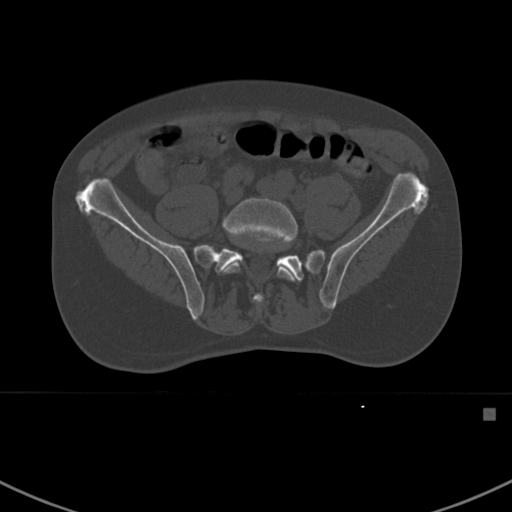
CT including the spine, one axial slice; slice 211 of 412 in the series (ordered by position); reconstruction kernel Br40s; 120 kVp; bone window (W 1800 / L 400 HU); 1.5 mm slice thickness; 512 × 512 image matrix. Patient: male, 59 years. Case-level facts recorded for this patient, not image findings: primary cancer: prostate.
Outlined on this slice (semi-automatic segmentation, software-assisted and operator-edited):
- L5 vertebra: box from (x=223, y=197) to (x=299, y=281) px